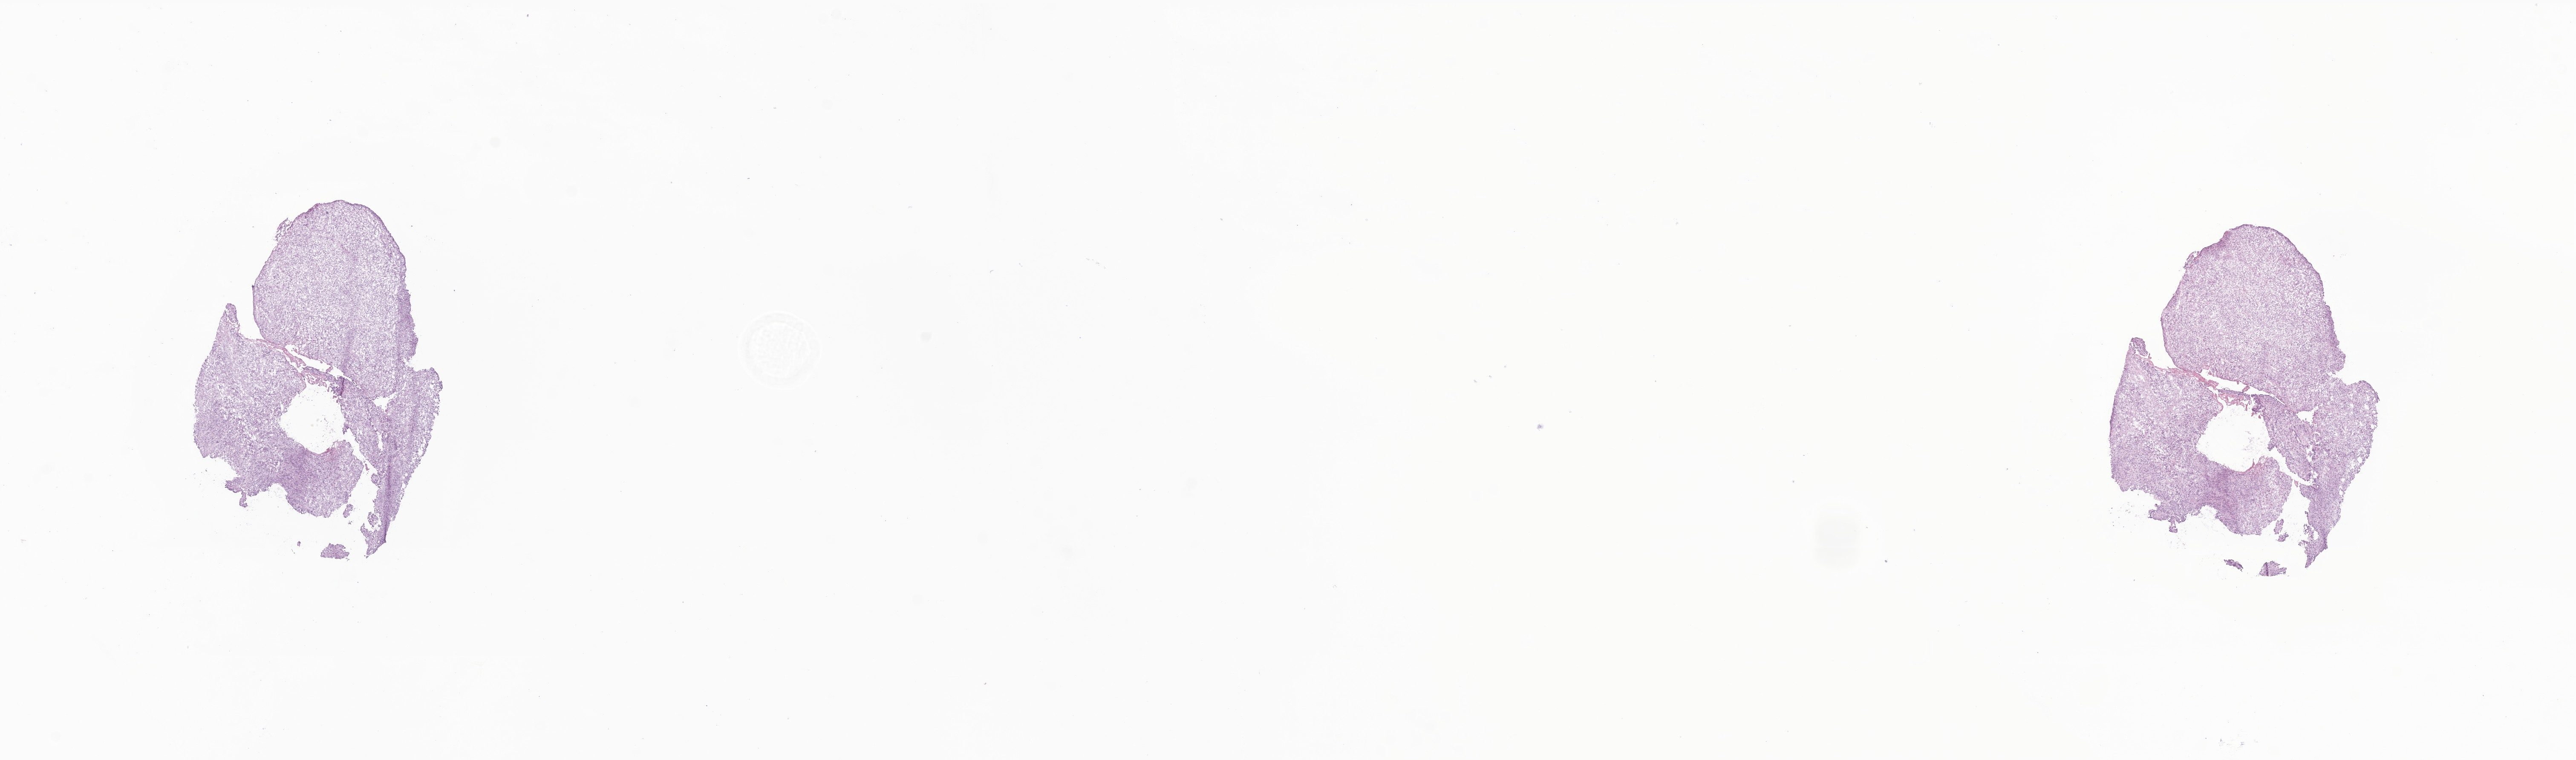
Whole-slide image, hematoxylin and eosin (H&E) stain of tumor tissue from the orbit, low-resolution overview of the scanned area, about 25.5 x 7.5 mm; cryosection (OCT / tissue freezing medium). Patient: male, age 149 months (12 years 5 months).
* recorded diagnosis: Rhabdomyosarcoma, NOS